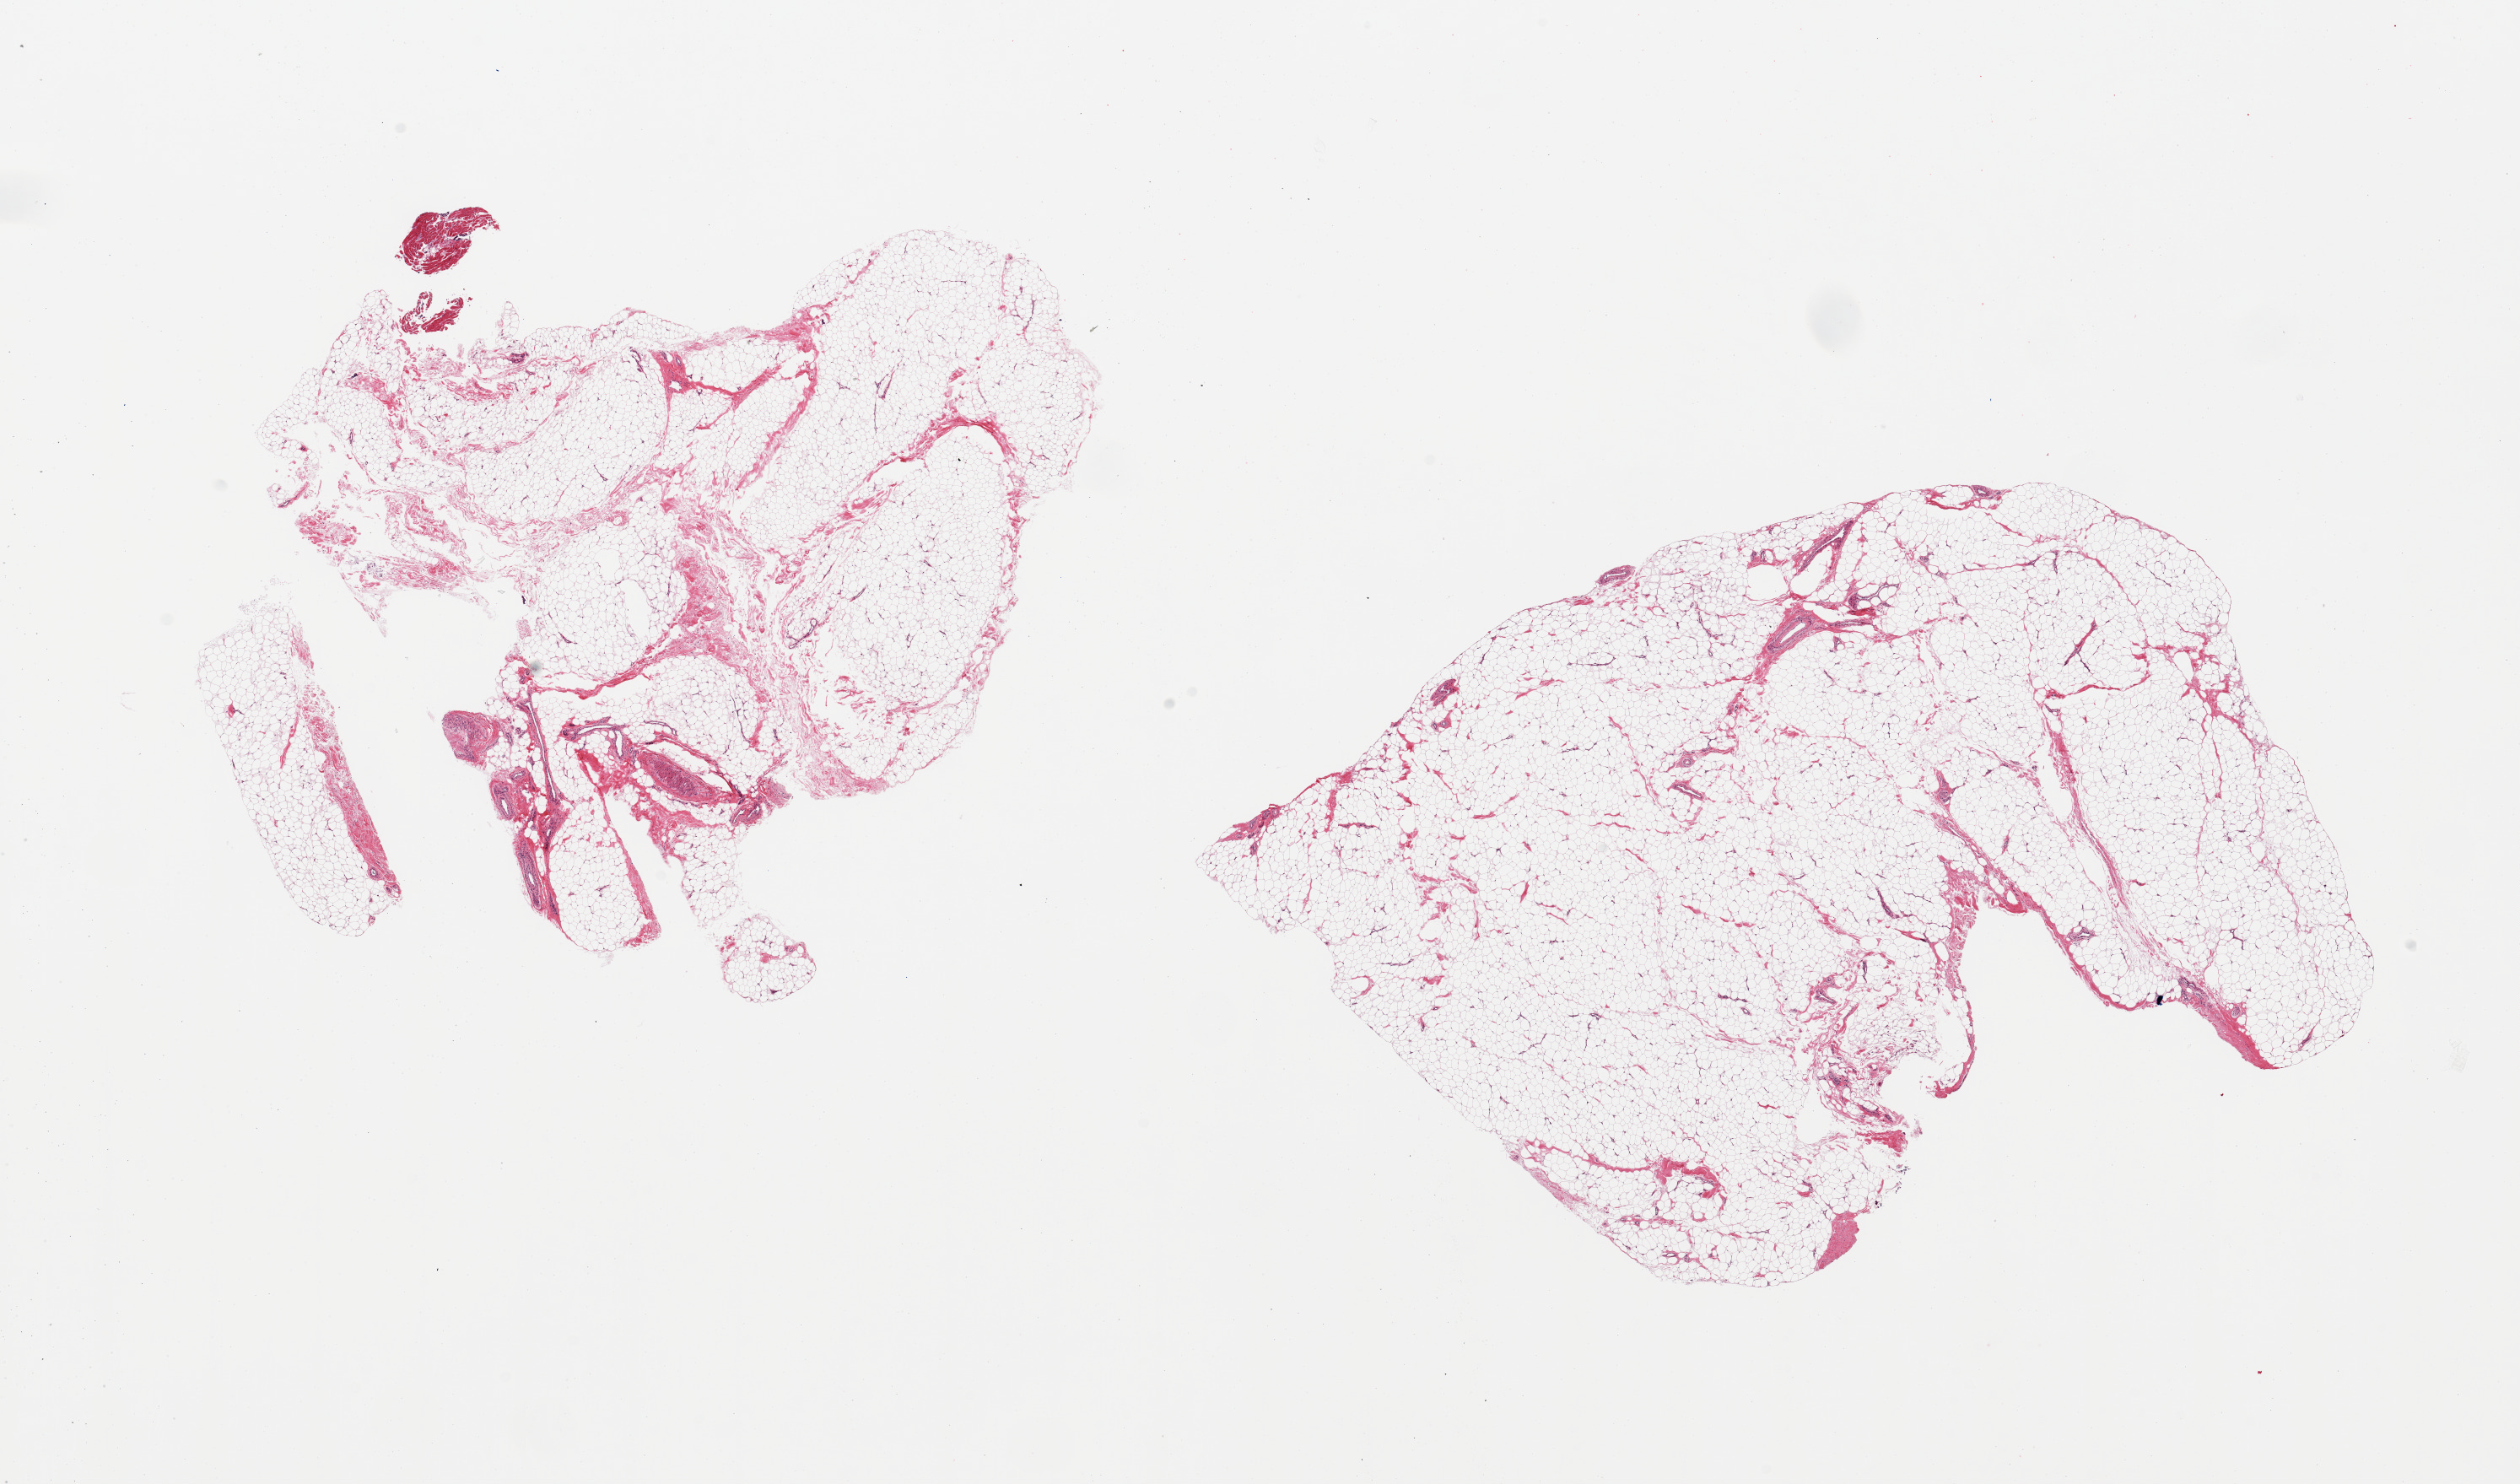
Digitized haematoxylin and eosin-stained section, brightfield, low-resolution overview of the scanned area, about 23.6 x 13.9 mm (acquisition: 20x scan), PAXgene-fixed paraffin-embedded (PFPE) section, target tissue: adipose tissue, tissue donor sample. Male donor.
Pathologist's review note for this sample: 2 pieces; small fragments of muscle on edge of 1 piece.